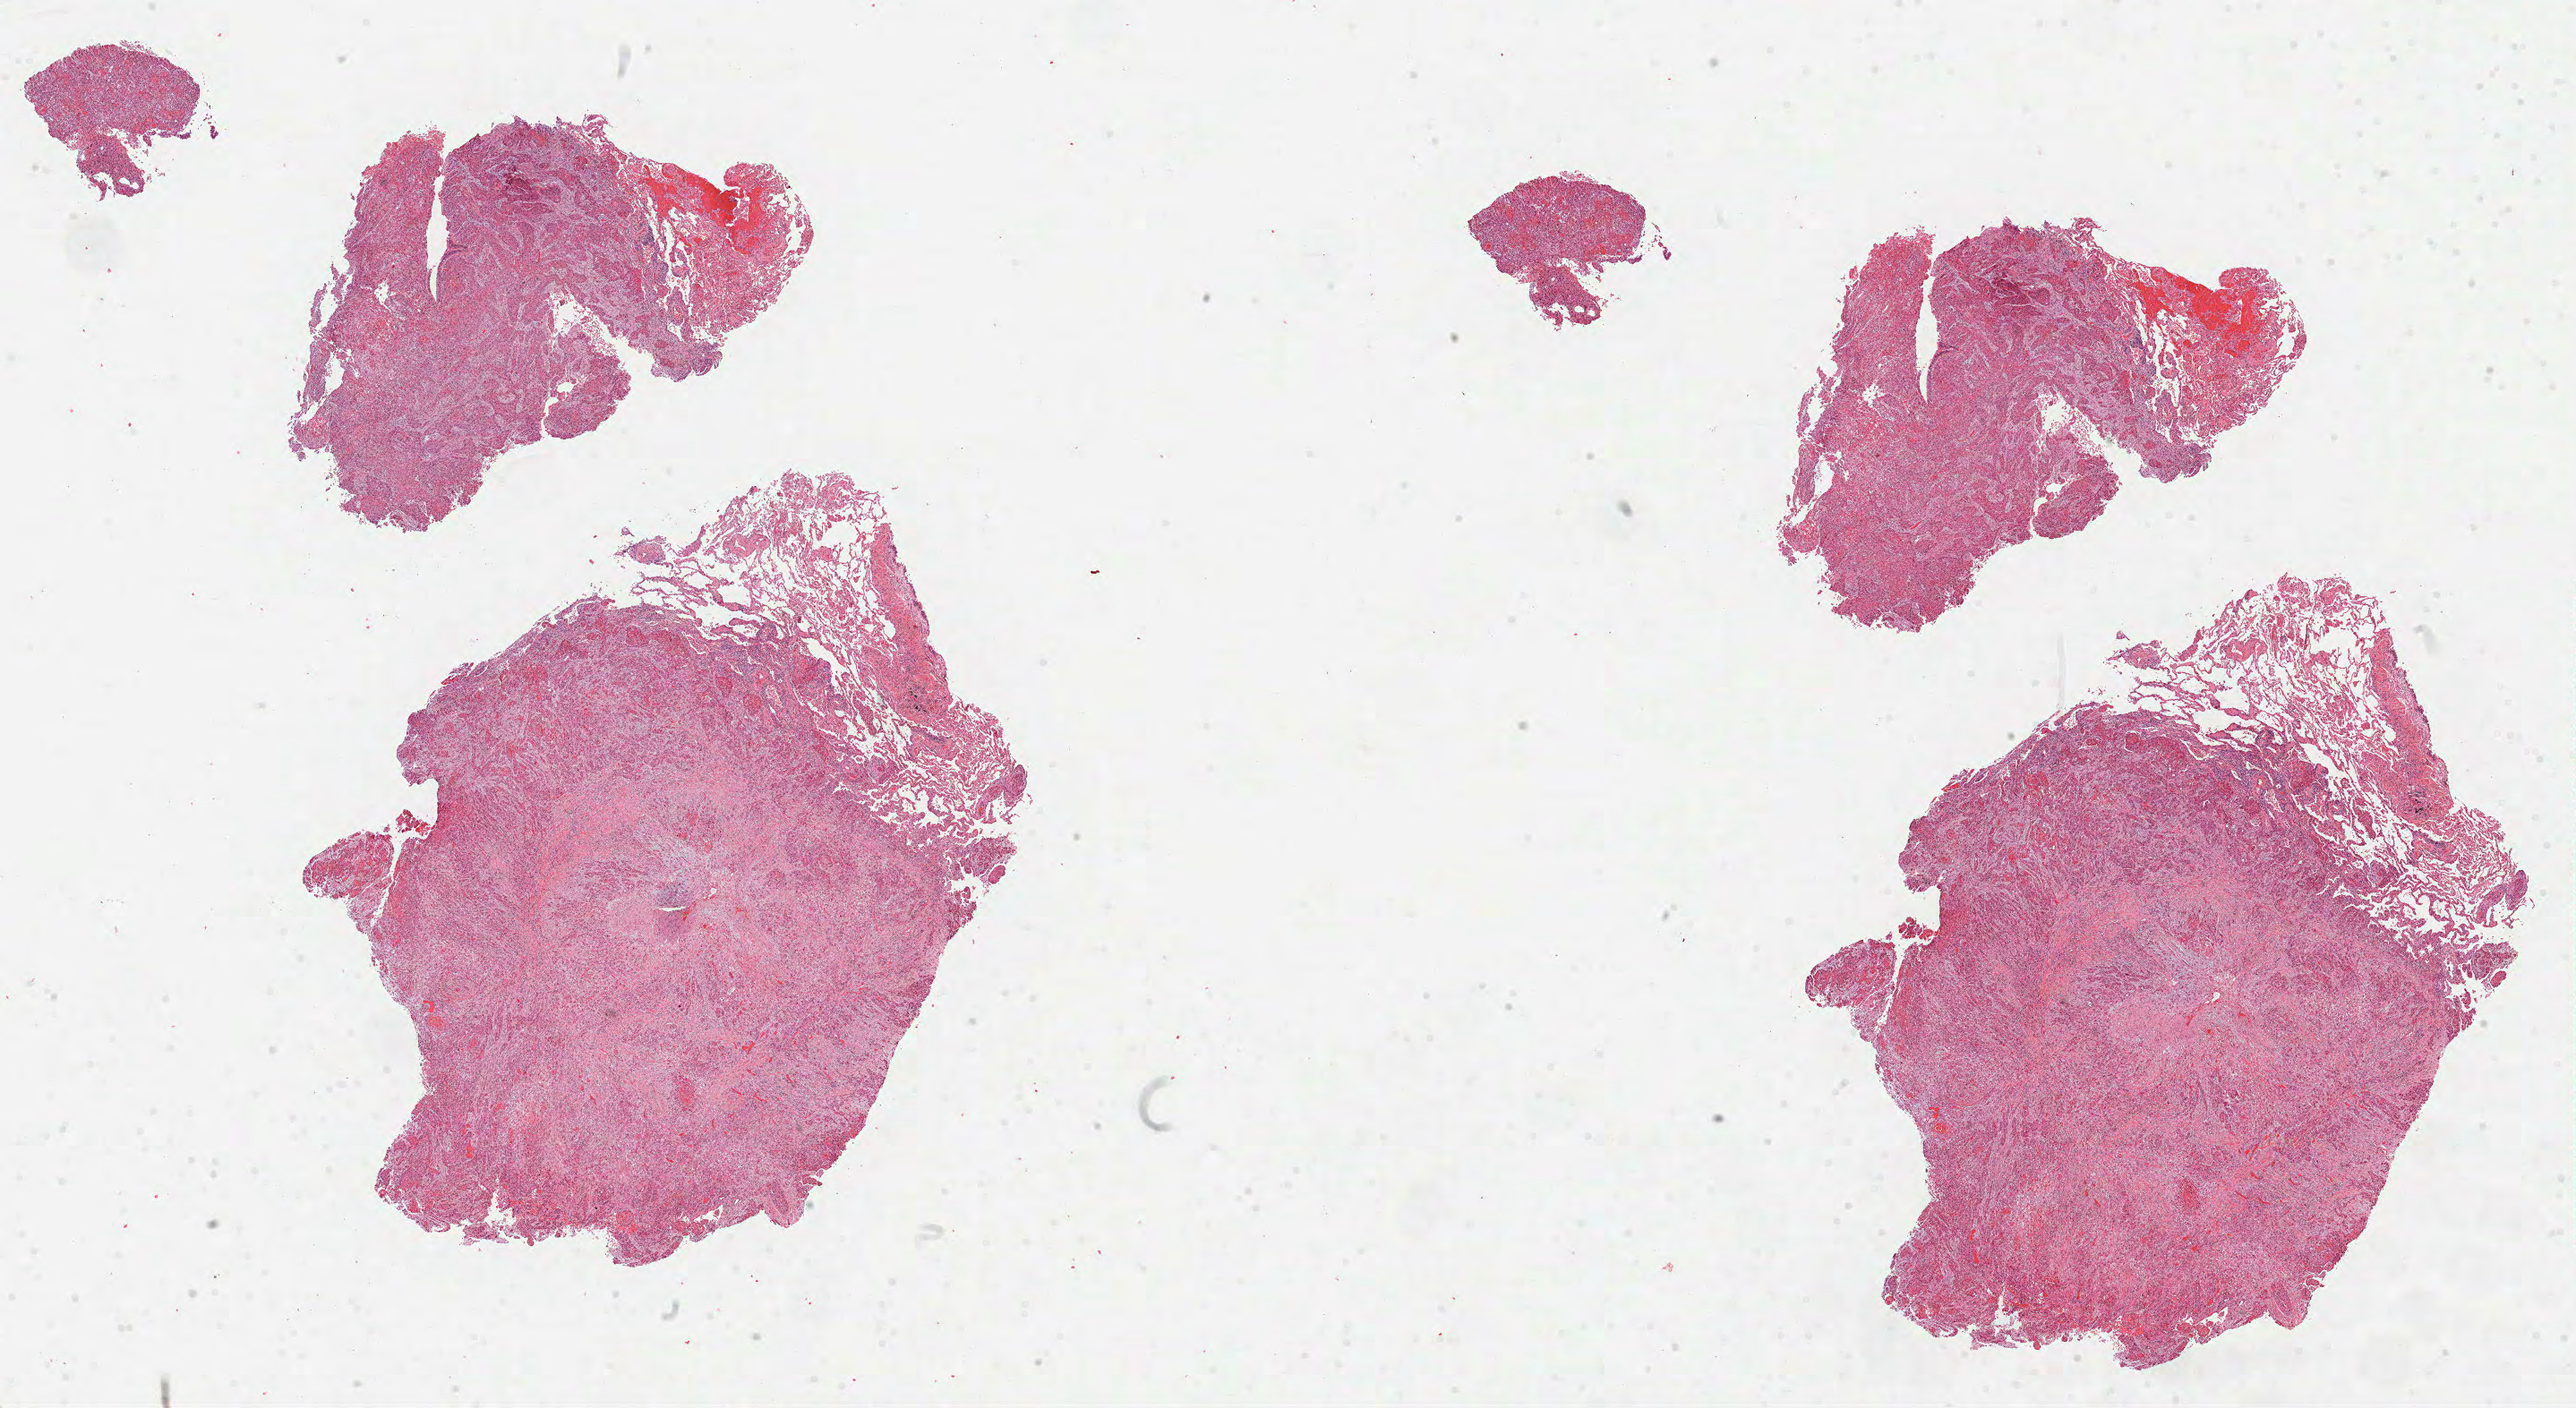
Whole-slide histology image, H&E, shown as a low-resolution overview of the whole scanned area (about 23.2 x 12.7 mm, from a 40x scan); FFPE section; lung, primary tumour sample. Female, age 56 years at initial diagnosis.
Pathologic diagnosis: Squamous cell carcinoma, NOS (upper lobe, lung).